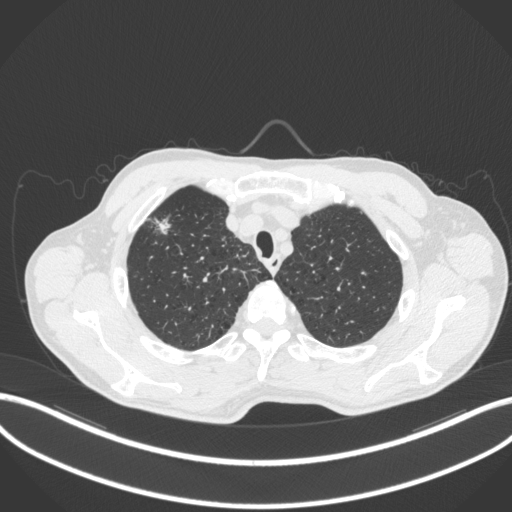
Chest CT, one axial slice. Position 357 of 414 along the scan axis. 120 kVp. Lung window (W 1500 / L -600 HU). 1 mm slice thickness. 512 × 512 image matrix, field of view 400 × 400 mm. Patient: male, 69 years. Case-level facts recorded for this patient, not image findings: clinical TNM (as recorded): T1b N1 M0.
Outlined on this slice (bounding box drawn by a radiologist):
- lung tumour (recorded histology: adenocarcinoma): bounding box [x1, y1, x2, y2] px = [153, 212, 175, 239]